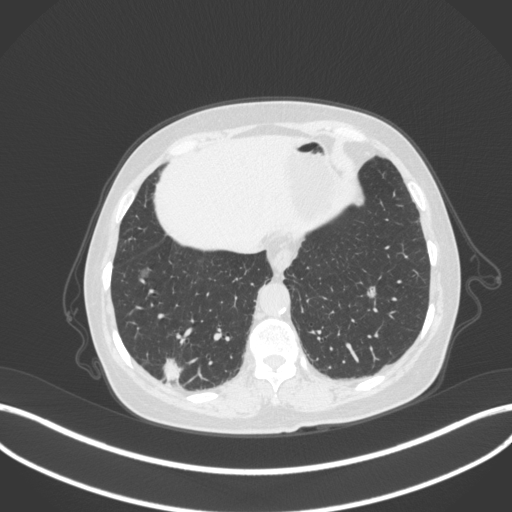
Chest CT, one axial slice. Slice 65 of 340 in the series (ordered by position). Reconstruction kernel B31f. 120 kVp. Lung window (W 1500 / L -600 HU). 1 mm slice thickness. 512 × 512 image matrix. Patient: female, 69 years. From the clinical record (not read from this slice): clinical TNM (as recorded): T1b N0 M0; histopathological grade: G2-3.
Outlined on this slice (bounding box drawn by a radiologist):
- lung tumour (recorded histology: adenocarcinoma): bounding box <161,353,183,386> (left, top, right, bottom; pixels)